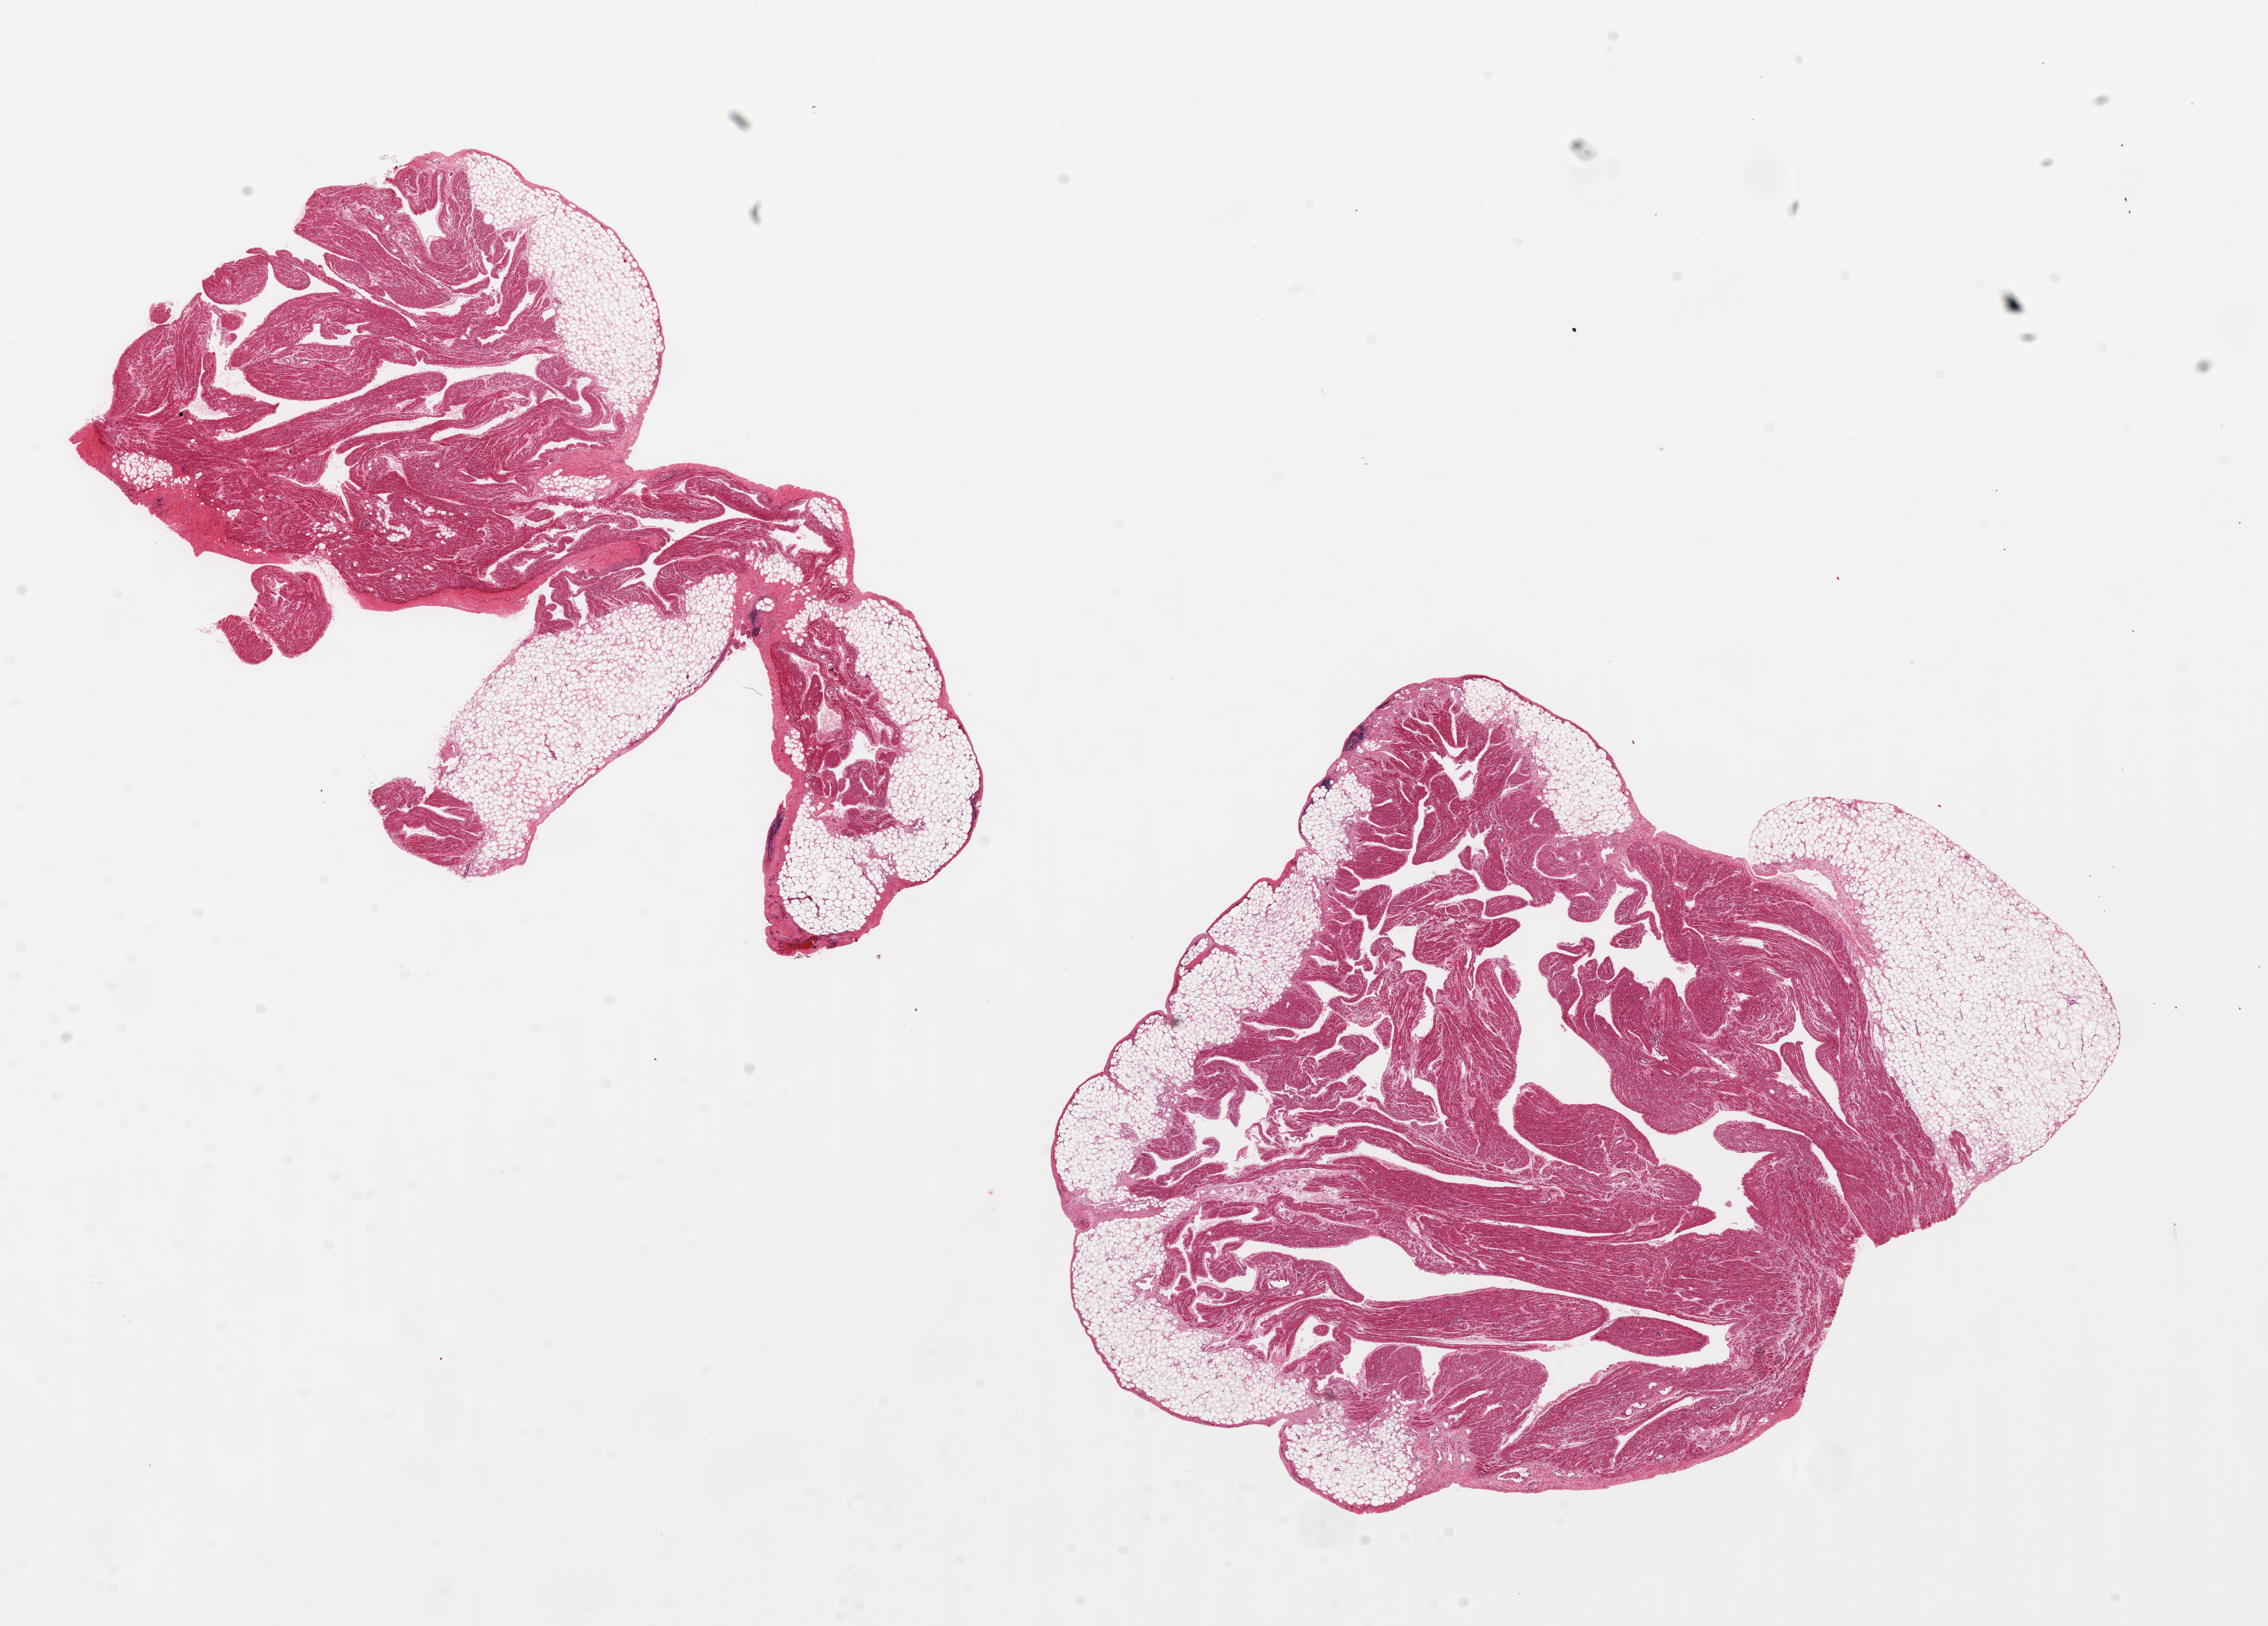
Digitized haematoxylin and eosin-stained section, low-resolution overview of the scanned area, about 23.6 x 16.9 mm. PAXgene-fixed paraffin-embedded (PFPE) section. Sampled site (target tissue): auricular appendage. Donor tissue sample.
- reviewer comment on this tissue sample: 2 pieces, 9x6 & 9x8mm; 20-30% surrounding adipose; should try to trim this